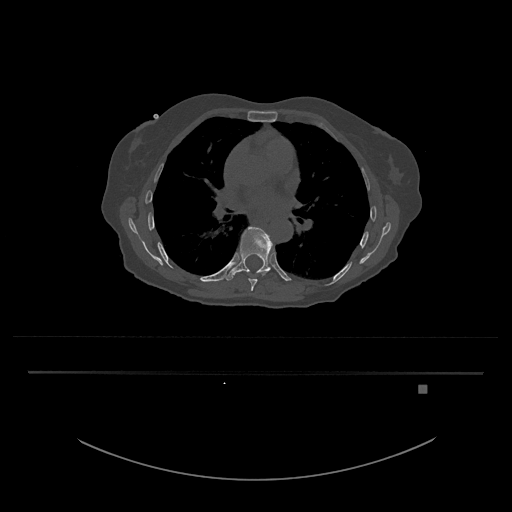
CT including the spine, one axial slice. Slice 778 of 797 in the series (ordered by position). Reconstruction kernel Br40s/3. 120 kVp. Bone window (W 1800 / L 400 HU). 0.5 mm slice thickness. 512 × 512 image matrix, field of view 500 × 500 mm. Female patient, age 57 years. Case-level facts recorded for this patient, not image findings: primary cancer: cervical.
Outlined on this slice (semi-automatic segmentation, software-assisted and operator-edited):
- T8 vertebra: bounding box <247,271,265,291> (left, top, right, bottom; pixels)
- T9 vertebra: <224,227,274,281>